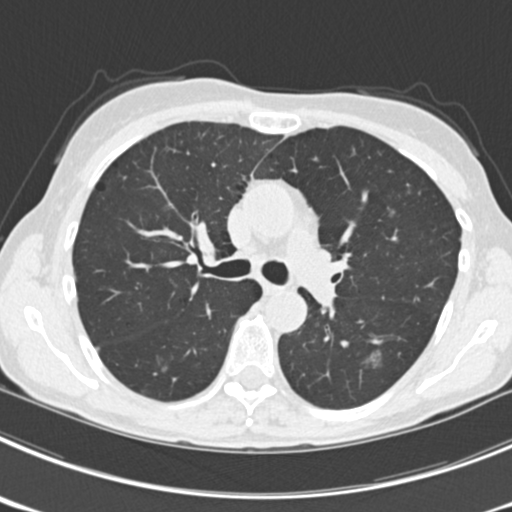
Chest CT (low-dose screening protocol), one axial image. Third annual screen. Lung window (W 1500 / L -600 HU). 2 mm slice thickness. 512 × 512 image matrix. Female, age 63 years at enrolment.
2 lesions marked by an expert reader on this slice (largest first), box from (x=131, y=331) to (x=179, y=381) px; (x=357, y=342)–(x=397, y=381). The screening reader recorded 9 non-calcified nodules or masses ≥4 mm on this exam; which of them these boxes mark is not recorded. Participant outcome: lung cancer diagnosed 15 days after this screen — bronchiolo-alveolar adenocarcinoma, NOS, right upper lobe, right middle lobe, right lower lobe, left upper lobe, left lower lobe, moderately differentiated (G2), stage IV (AJCC 6th edition).